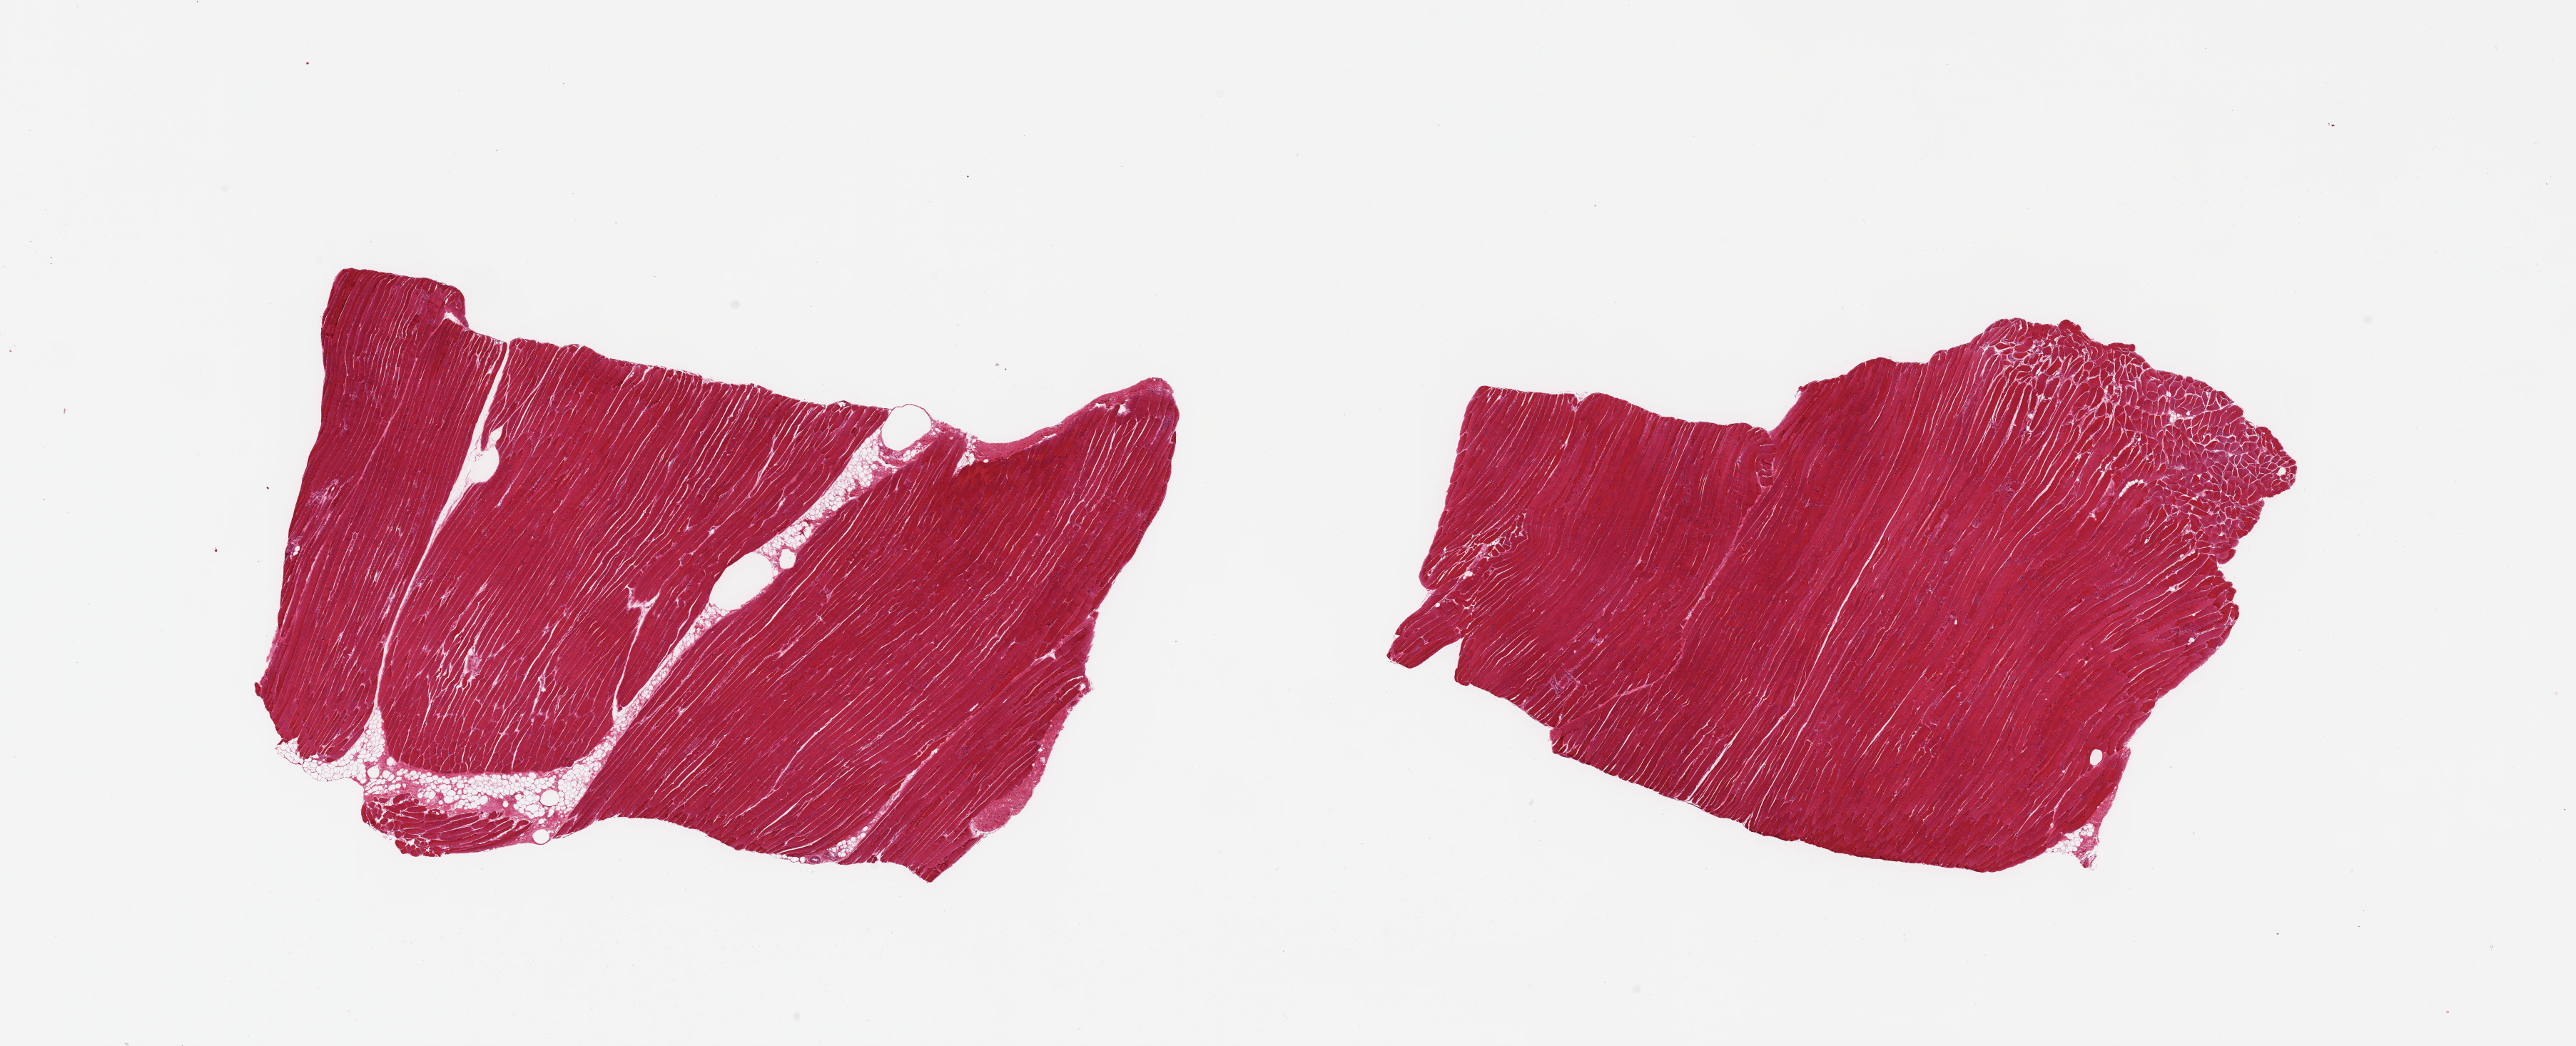
H&E whole-slide image, brightfield, a low-resolution overview of the entire scanned area, about 28.5 x 11.6 mm (slide scanned at 20x); PAXgene-fixed, paraffin-embedded tissue; section of skeletal muscle (target tissue); tissue donor sample. Donor sex: male.
Review note (as recorded): 2 pieces; 1 with 5% internal fat.